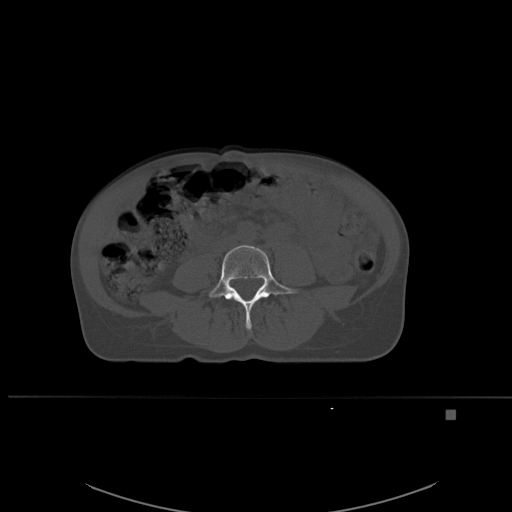
CT including the spine, one axial slice. Bone window (W 1800 / L 400 HU). 512 × 512 image matrix. Female patient, age 45 years. Case-level facts recorded for this patient, not image findings: primary cancer: lung.
Outlined on this slice (semi-automatic segmentation, software-assisted and operator-edited):
- L4 vertebra: bounding box <208,245,298,330> (left, top, right, bottom; pixels)